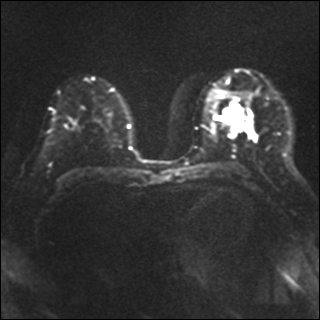
Breast MRI, one axial slice; position 21 of 40 along the scan axis; diffusion-weighted series; image 2 of 4 stored at this slice position (different b-values; order by instance number); 1.5 T; 320 × 320 image matrix. Female patient.
Outlined on this slice (outlined manually by an expert reader):
- tumour on diffusion-weighted imaging: box from (x=231, y=108) to (x=248, y=130) px